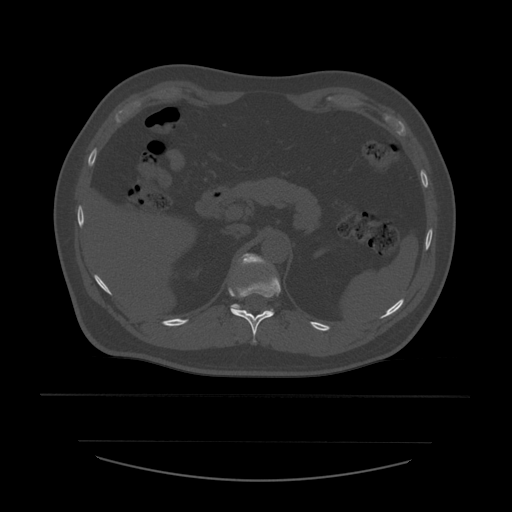
CT including the spine, one axial slice. Reconstruction kernel STANDARD. Bone window (W 1800 / L 400 HU). 1.25 mm slice thickness. 512 × 512 image matrix, field of view 441 × 441 mm. Patient age 44 years. From the clinical record (not read from this slice): primary cancer: soft tissue sarcoma.
Annotated regions visible in this slice (semi-automatic segmentation, software-assisted and operator-edited):
- T11 vertebra: bounding box (x1, y1, x2, y2) in pixels: (231, 266, 281, 343)
- T12 vertebra: (229, 254, 264, 310)